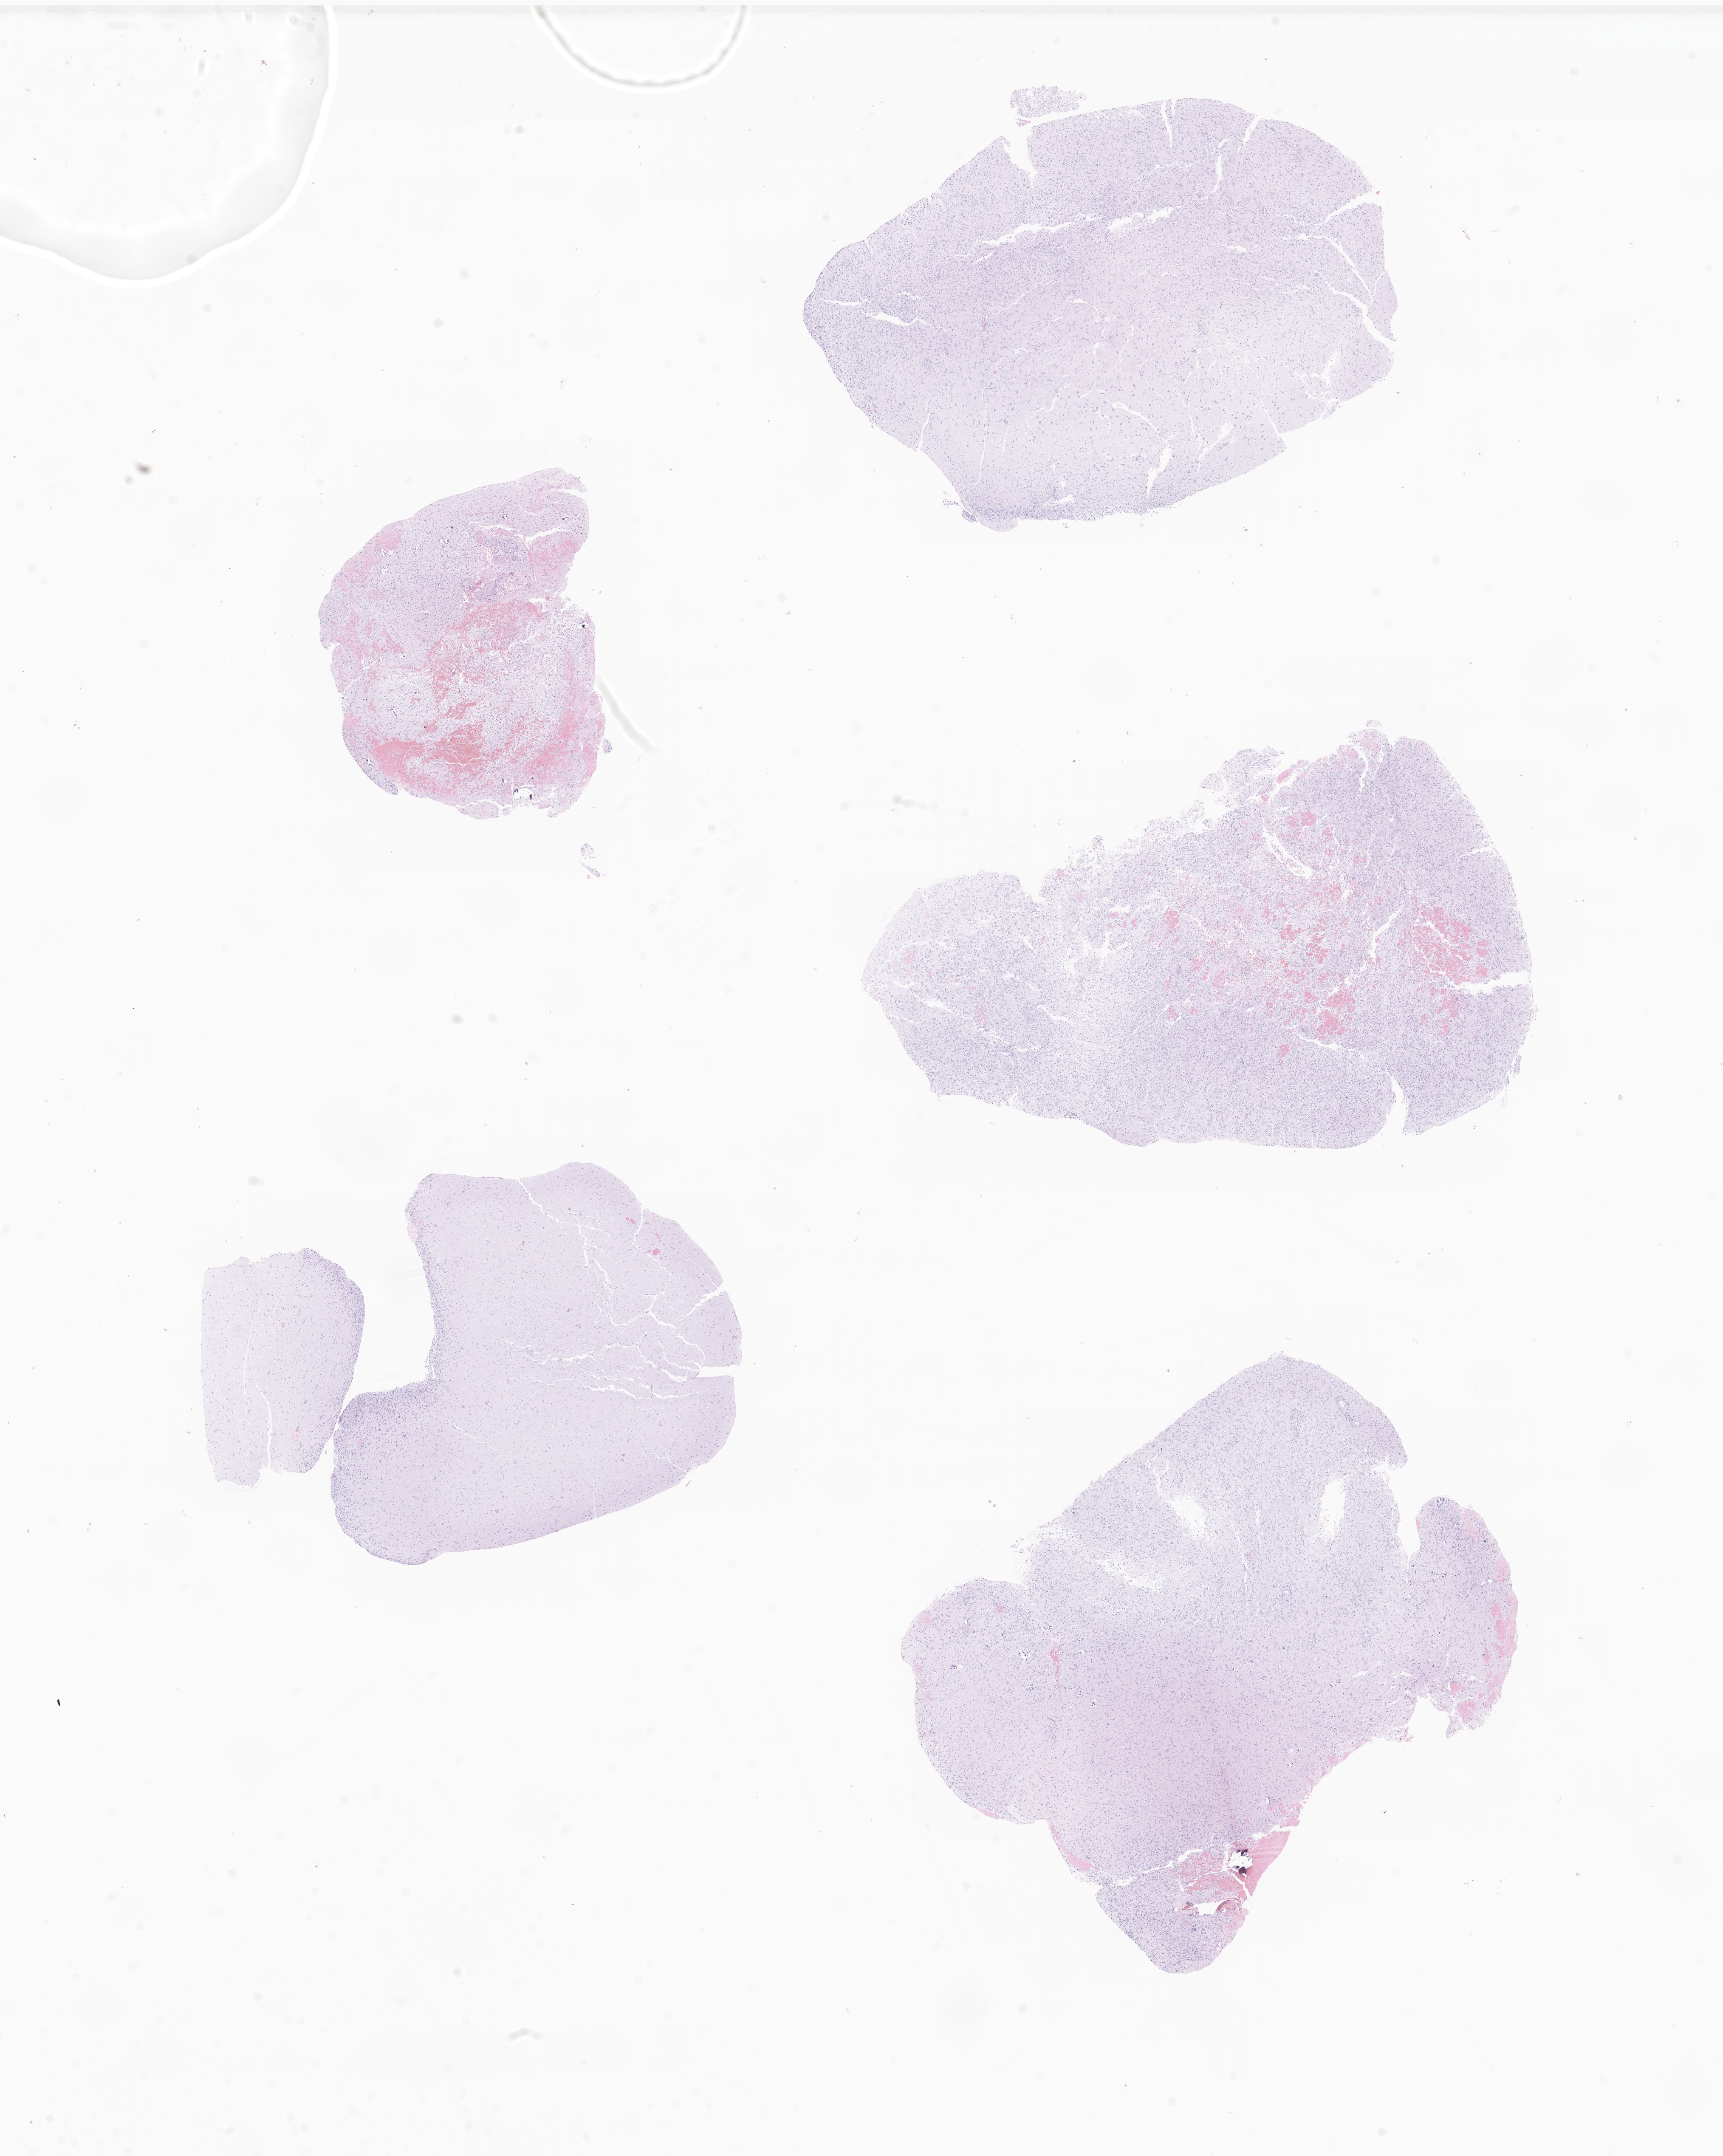
Digitized haematoxylin and eosin-stained section of tumor tissue from the brain, shown as a low-resolution overview of the whole scanned area (about 17.1 x 21.4 mm). Formalin-fixed paraffin-embedded section. Female patient, age 108 months (9 years).
* diagnosis: Neoplasm, uncertain whether benign or malignant